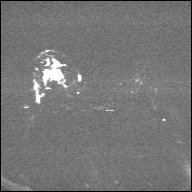
Breast MRI, one axial slice; diffusion-weighted series; image 2 of 4 stored at this slice position (different b-values; order by instance number); 1.5 T; 4 mm slice thickness; 192 × 192 image matrix, field of view 360 × 360 mm. Female patient.
Annotated regions visible in this slice (manually delineated by an expert):
- tumour on diffusion-weighted imaging: box from (x=48, y=69) to (x=59, y=78) px